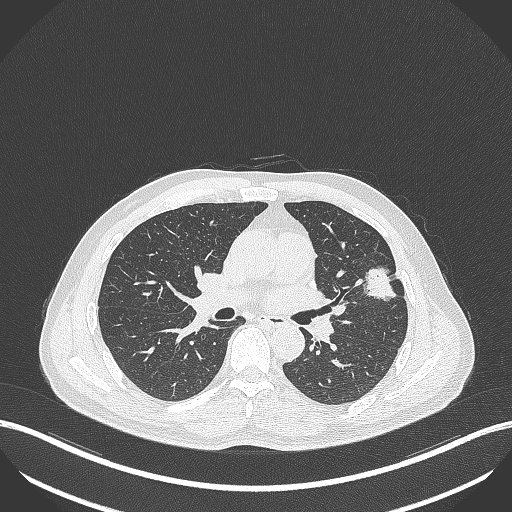
Chest CT, one axial slice. Slice 221 of 418 in the series (ordered by position). Reconstruction kernel B70f. Lung window (W 1500 / L -600 HU). 1 mm slice thickness. 512 × 512 image matrix, field of view 400 × 400 mm. Patient: male, 55 years. From the clinical record (not read from this slice): clinical TNM (as recorded): T1c N0 M0; histopathological grade: G2-3.
Annotated regions visible in this slice (rectangle marked by the reading radiologist):
- lung tumour (recorded histology: adenocarcinoma): bounding box [x1, y1, x2, y2] px = [359, 261, 401, 300]